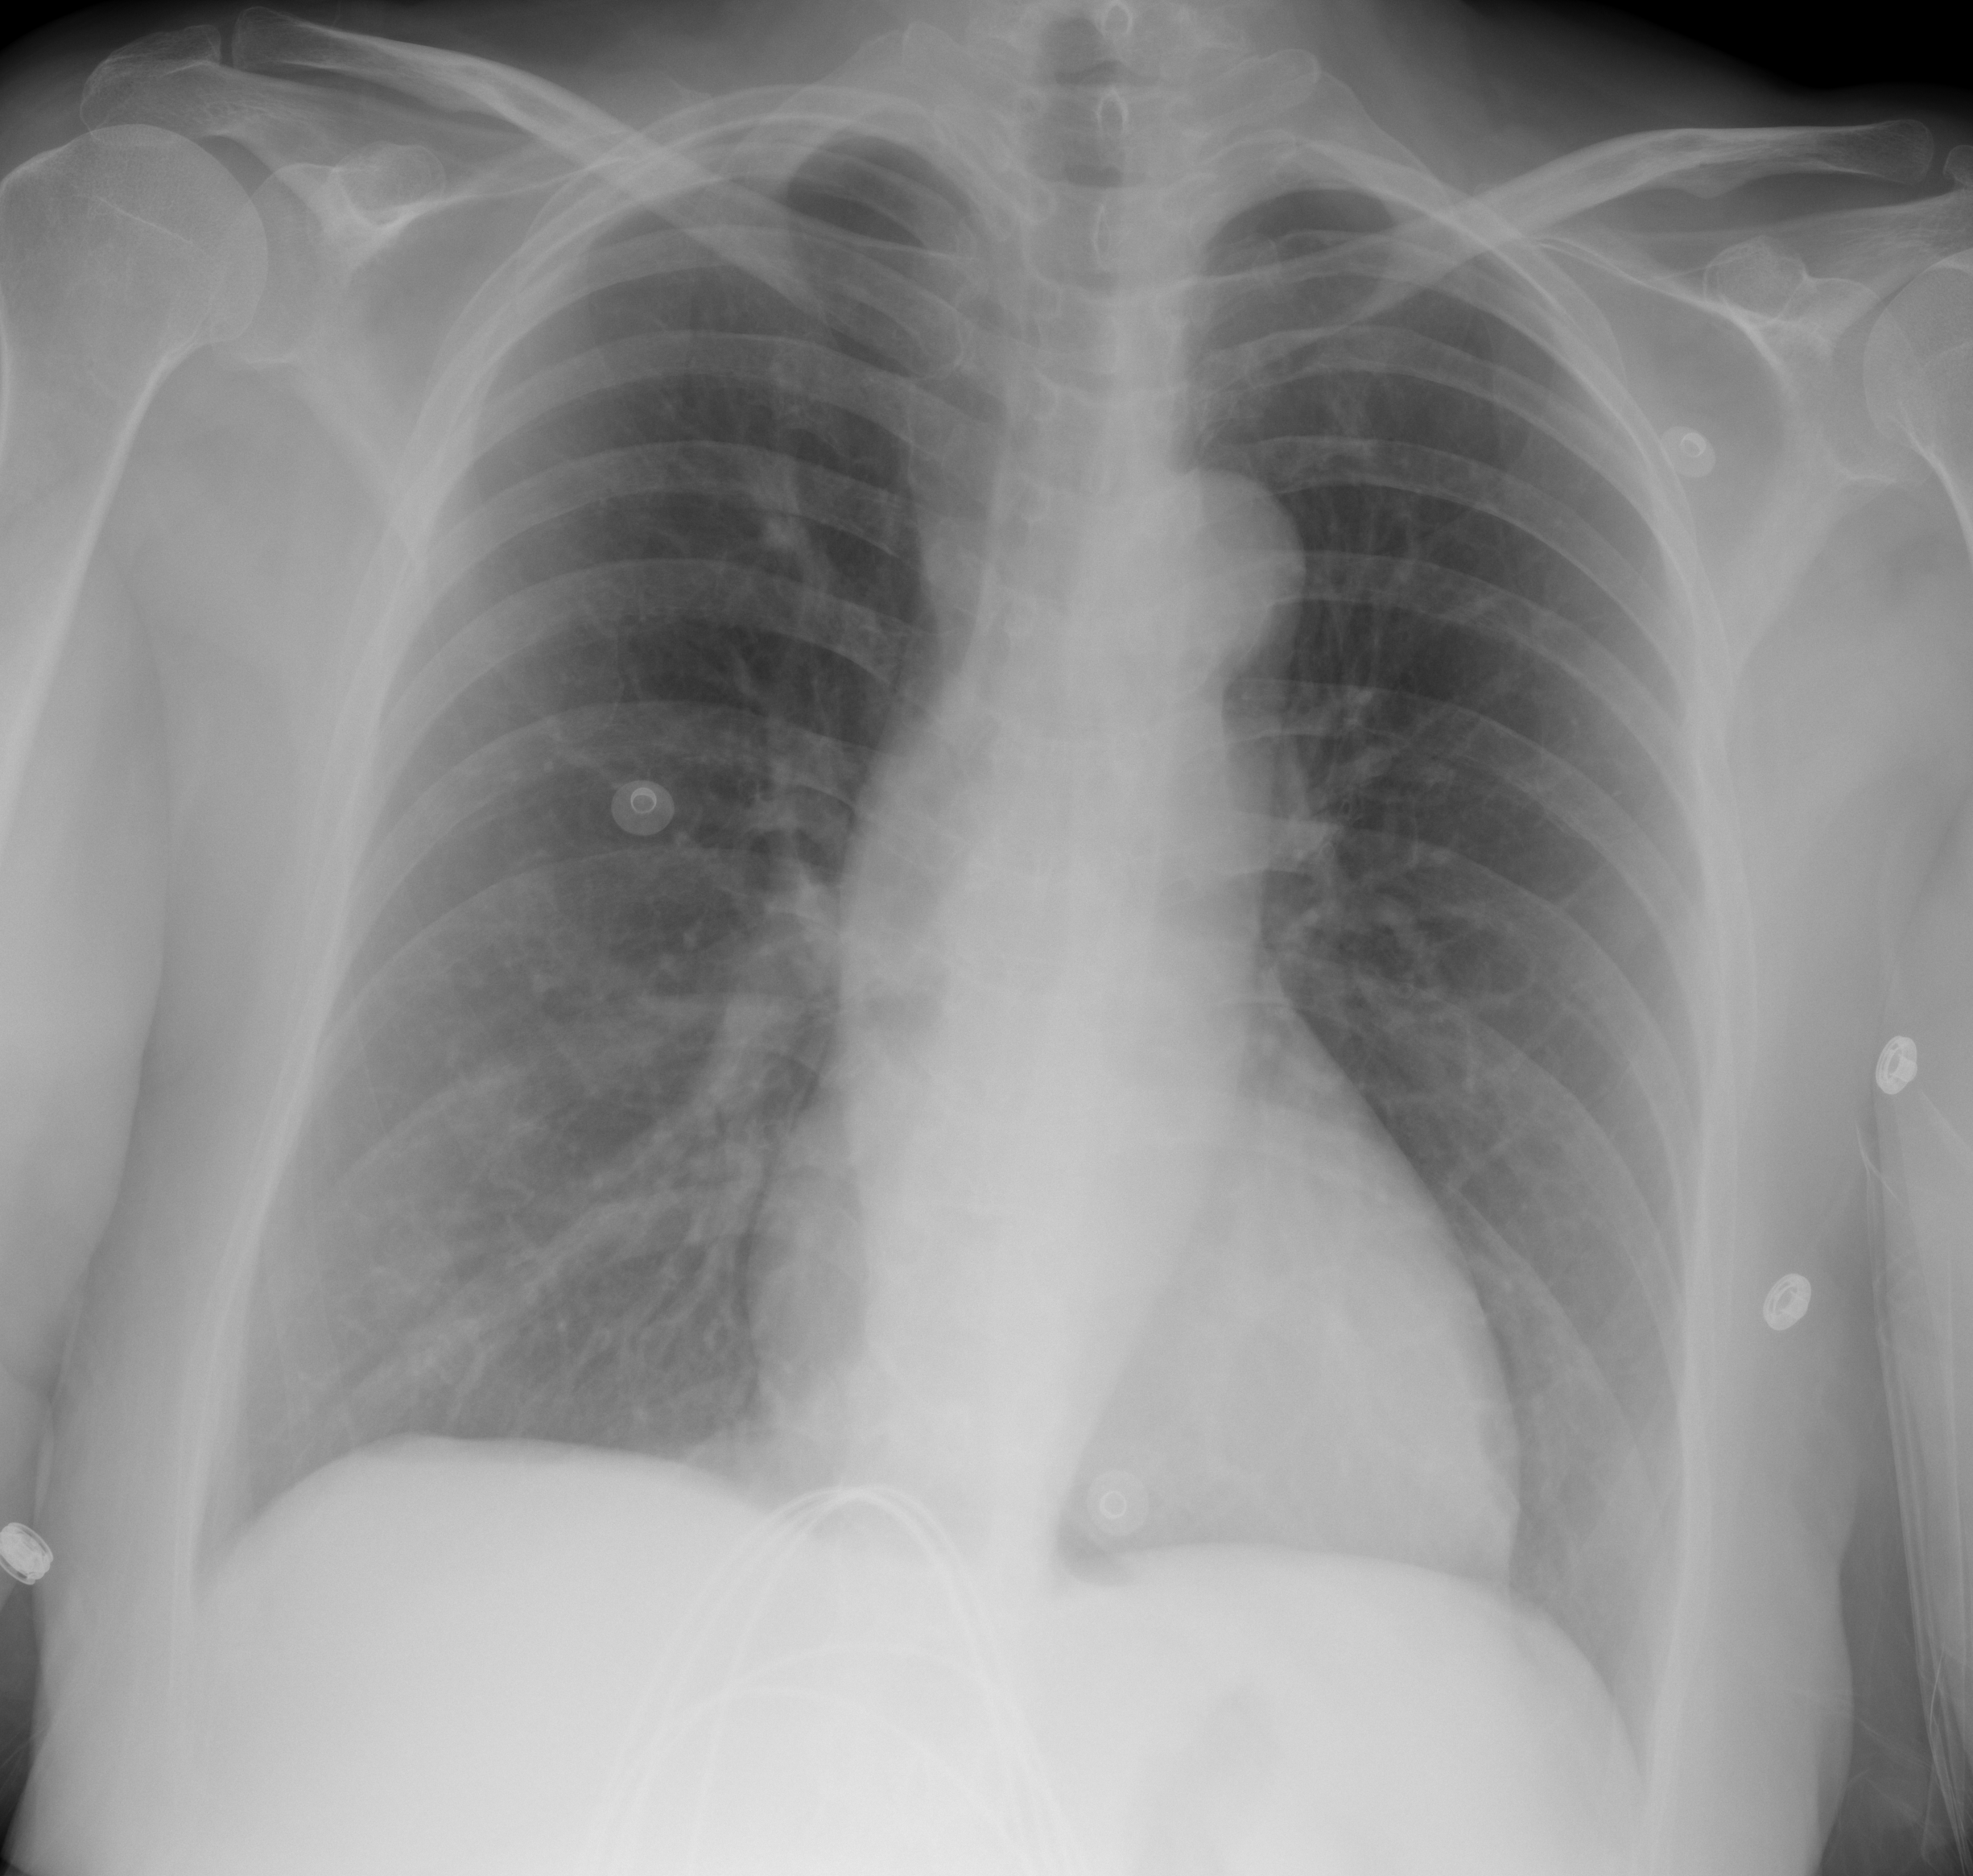
Chest X-ray (portable), AP projection. Female patient, age 59 years; imaged 3 days after the COVID-19 diagnosis.
Radiologist's key findings for this exam: The lungs are clear.